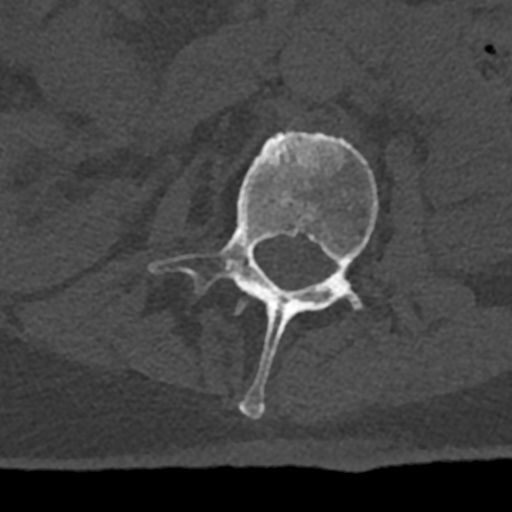
CT including the spine, one axial slice; position 377 of 797 along the scan axis; reconstruction kernel Br40s/3; bone window (W 1800 / L 400 HU); 0.5 mm slice thickness; 512 × 512 image matrix. Patient: male, 74 years. Case-level facts recorded for this patient, not image findings: primary cancer: renal.
Annotated regions visible in this slice (semi-automatic segmentation, software-assisted and operator-edited):
- L1 vertebra: bounding box (x1, y1, x2, y2) in pixels: (236, 301, 245, 314)
- L2 vertebra: (148, 130, 378, 418)